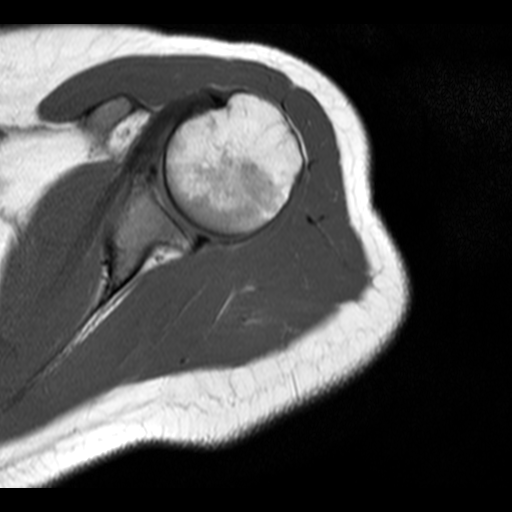
MRI of an extremity soft-tissue mass, one axial slice. Slice 14 of 20 in the series (ordered by position). 4 mm slice thickness. 512 × 512 image matrix. Female patient. From the clinical record (not read from this slice): histological type: malignant fibrous histiocytoma; grade: low; site of the primary tumour: left arm.
Outlined on this slice (outlined manually by an expert reader):
- gross tumour volume (mass): bounding box [x1, y1, x2, y2] px = [222, 299, 271, 325]